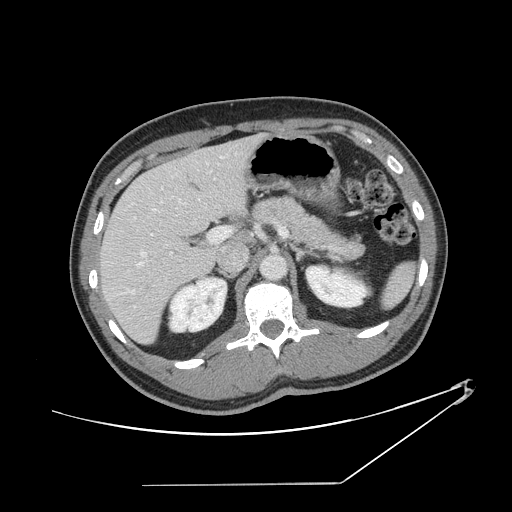
Contrast-enhanced abdominal CT, one axial slice. Position 82 of 152 along the scan axis. Intravenous contrast given. Soft-tissue window (W 400 / L 40 HU). 512 × 512 image matrix, field of view 432 × 432 mm. Male patient, age 45 years. From the clinical record (not read from this slice): diagnosis: colorectal cancer liver metastases, imaged before liver resection; multiple liver metastases: no; largest metastasis: 1 cm.
Outlined on this slice (manually delineated by an expert):
- hepatic veins: bounding box <129,156,225,294> (left, top, right, bottom; pixels)
- liver: <101,137,259,343>
- planned liver remnant (the part of the liver to remain after resection): <101,156,216,343>
- portal vein (with intrahepatic branches): <137,227,287,266>